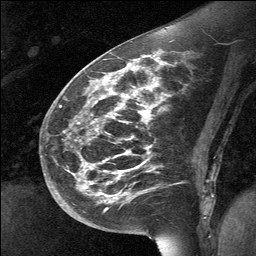
Breast MRI (dynamic contrast-enhanced), one sagittal slice. Slice 28 of 64 in the series (ordered by position). Dynamic contrast-enhanced study with each time point stored as its own series, time point 2 of 3 at this slice position (early post-contrast, ordered by acquisition time). 1.5 T. TE 4.8 ms, TR 27 ms. 2 mm slice thickness. 256 × 256 image matrix, field of view 200 × 200 mm. Patient: female, 39 years. From the clinical record (not read from this slice): setting: breast cancer imaged before/during neoadjuvant chemotherapy; receptor status: HER2-positive.
Structures marked on this image (semi-automatic segmentation, software-assisted and operator-edited):
- analysis volume of interest (the breast-tissue region the enhancement analysis was run in; not a lesion): bounding box [x1, y1, x2, y2] px = [70, 69, 164, 224]
- tumour enhancement mask (voxels above the 90 % enhancement threshold inside the analysis volume of interest): [105, 69, 139, 167]